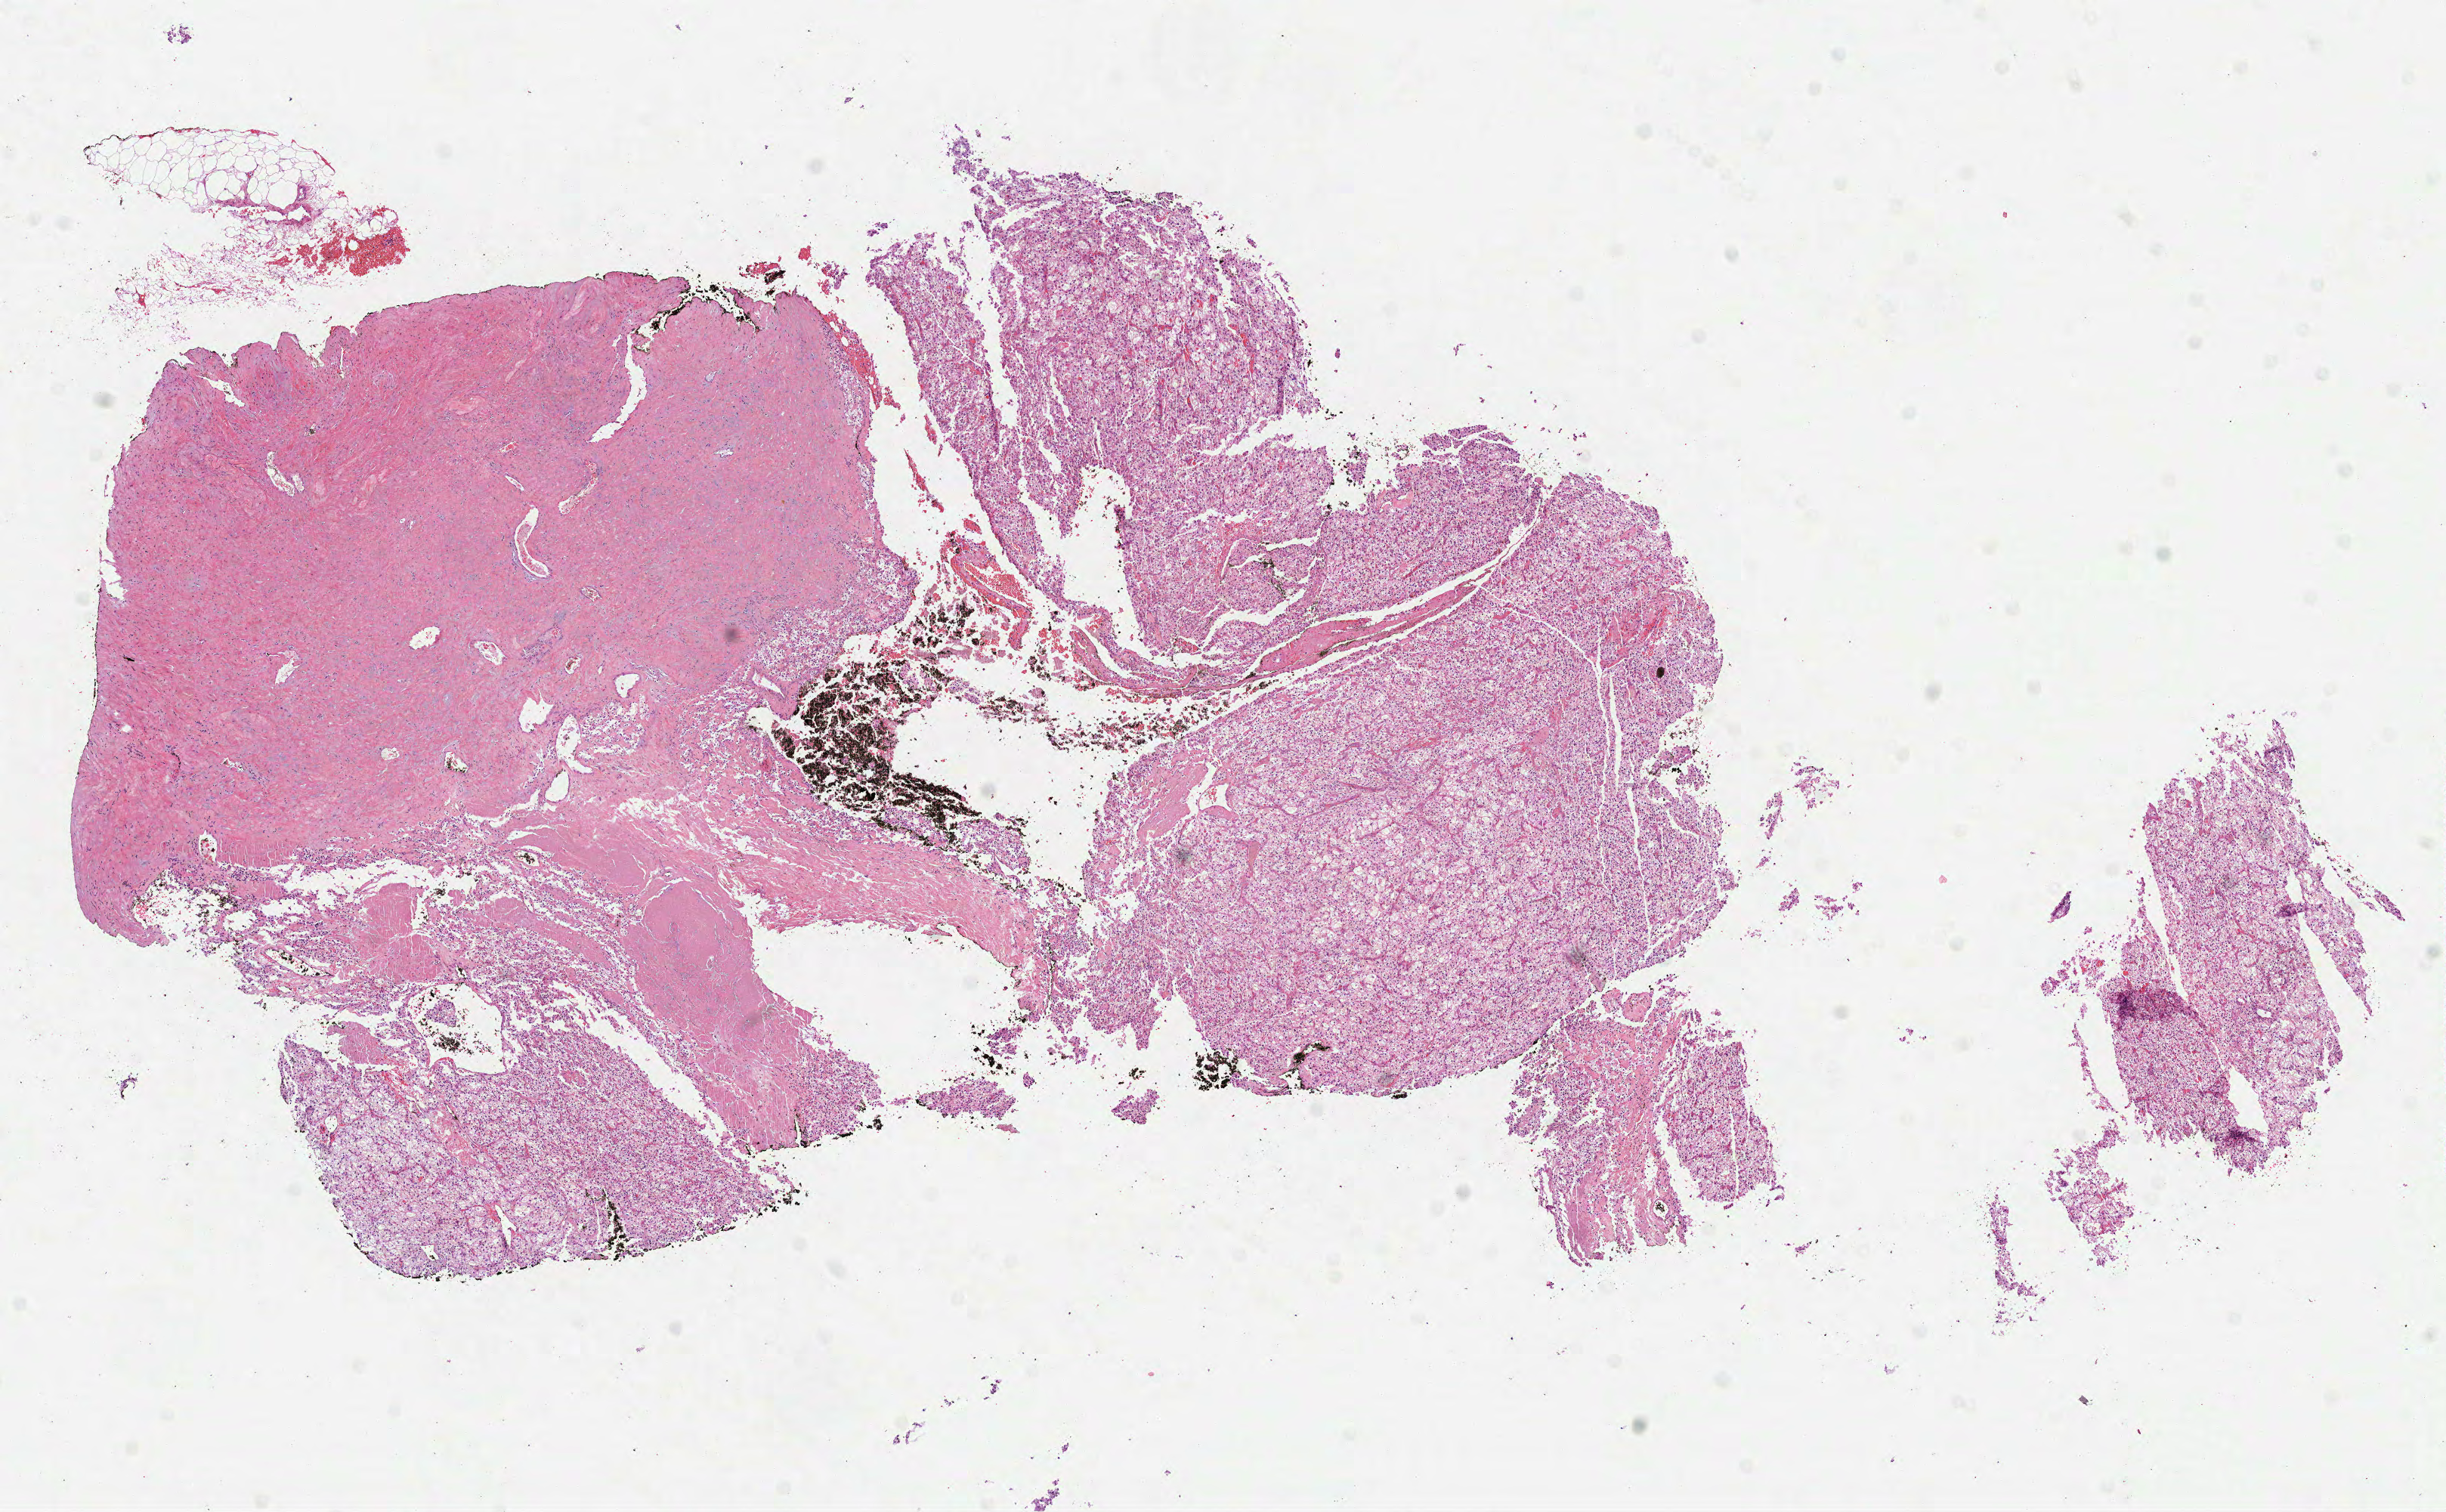
Digitized Hematoxylin and eosin (H&E) stained tissue section (whole slide) — a low-resolution overview of the entire scanned area, about 13.1 x 8.1 mm (from a 40x scan). Formalin-fixed paraffin-embedded (FFPE) diagnostic section. Sample: primary tumour, kidney. Patient: male, age at initial diagnosis 69 years. Histologic grade: G3 (poorly differentiated).
AJCC pathologic stage: I. Histologic diagnosis: Clear cell adenocarcinoma, NOS. Laterality: left.